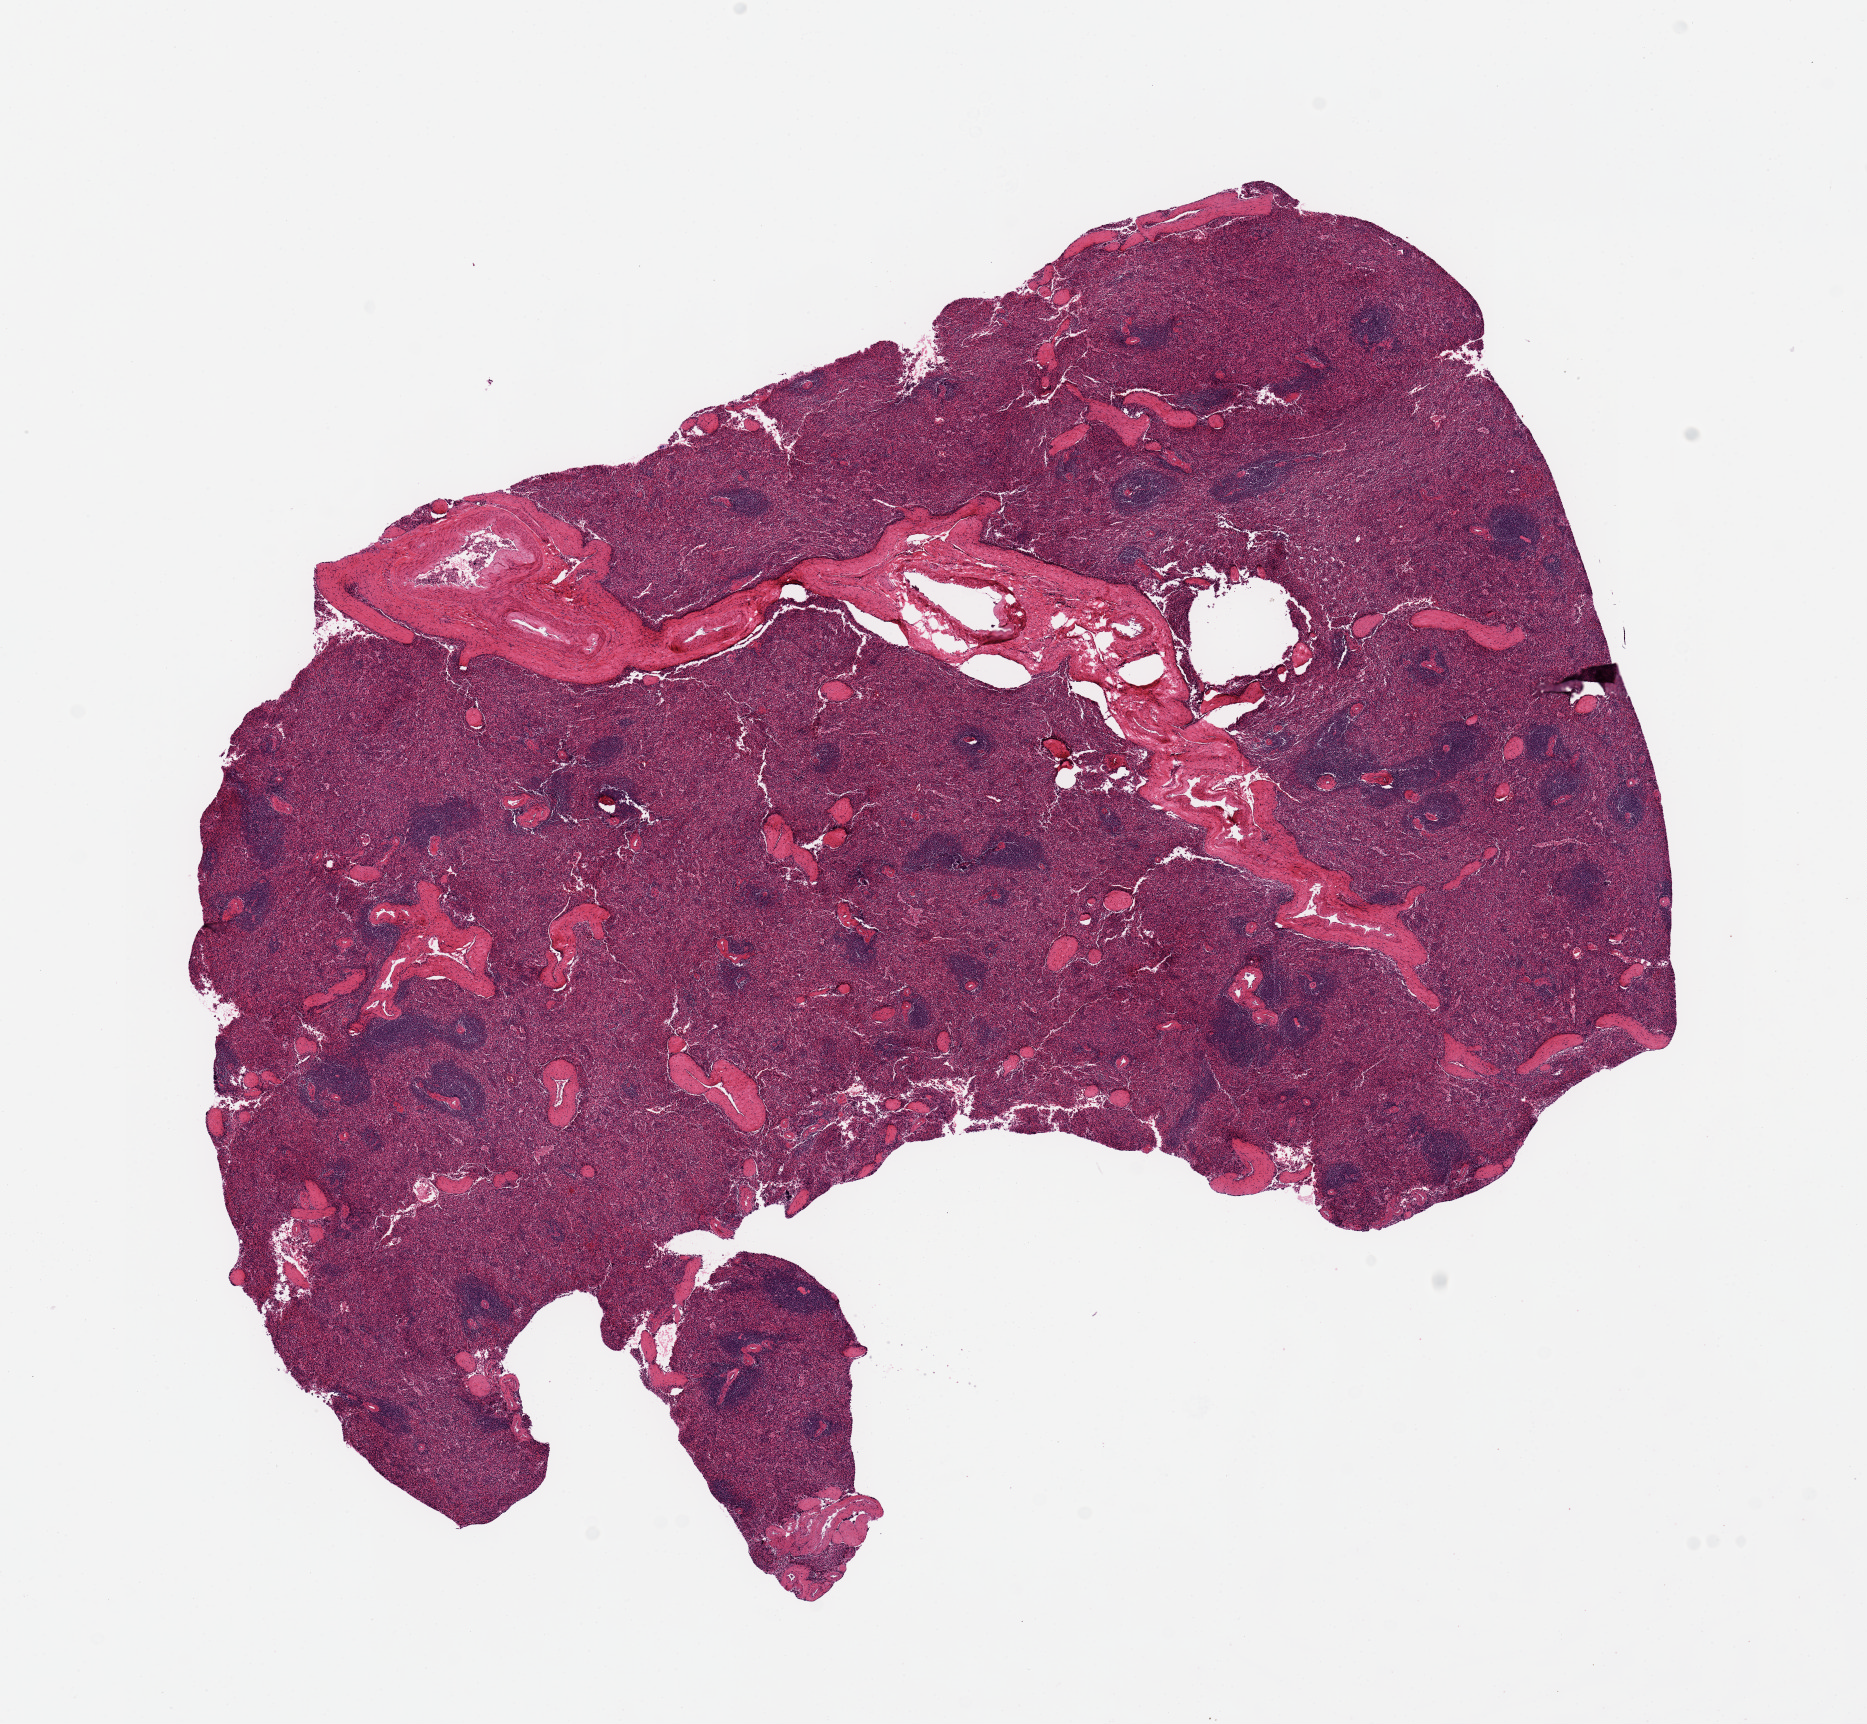
Haematoxylin and eosin whole-slide image — low-resolution overview of the scanned area, about 14.8 x 13.6 mm; PAXgene-fixed paraffin-embedded (PFPE) section; target tissue: spleen; donor tissue sample.
Review note (as recorded): 11.8 x 6.2 mm specimen.